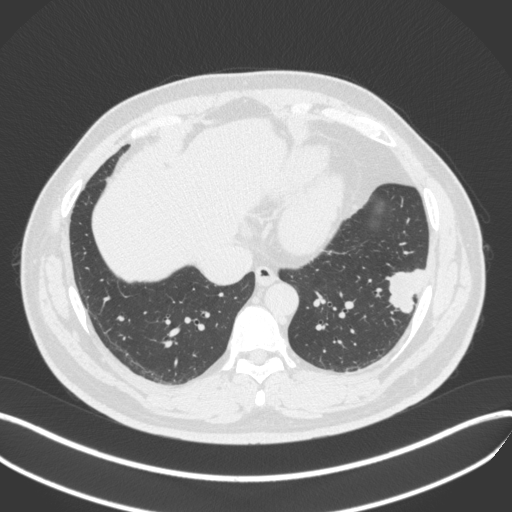
Chest CT, one axial slice; slice 131 of 420 in the series (ordered by position); 120 kVp; lung window (W 1500 / L -600 HU); 1 mm slice thickness; 512 × 512 image matrix, field of view 400 × 400 mm. Patient: male, 39 years. From the clinical record (not read from this slice): clinical TNM (as recorded): T2a N0 M0; histopathological grade: G2-3.
Outlined on this slice (bounding box drawn by a radiologist):
- lung tumour (recorded histology: adenocarcinoma): bounding box [x1, y1, x2, y2] px = [383, 264, 429, 322]